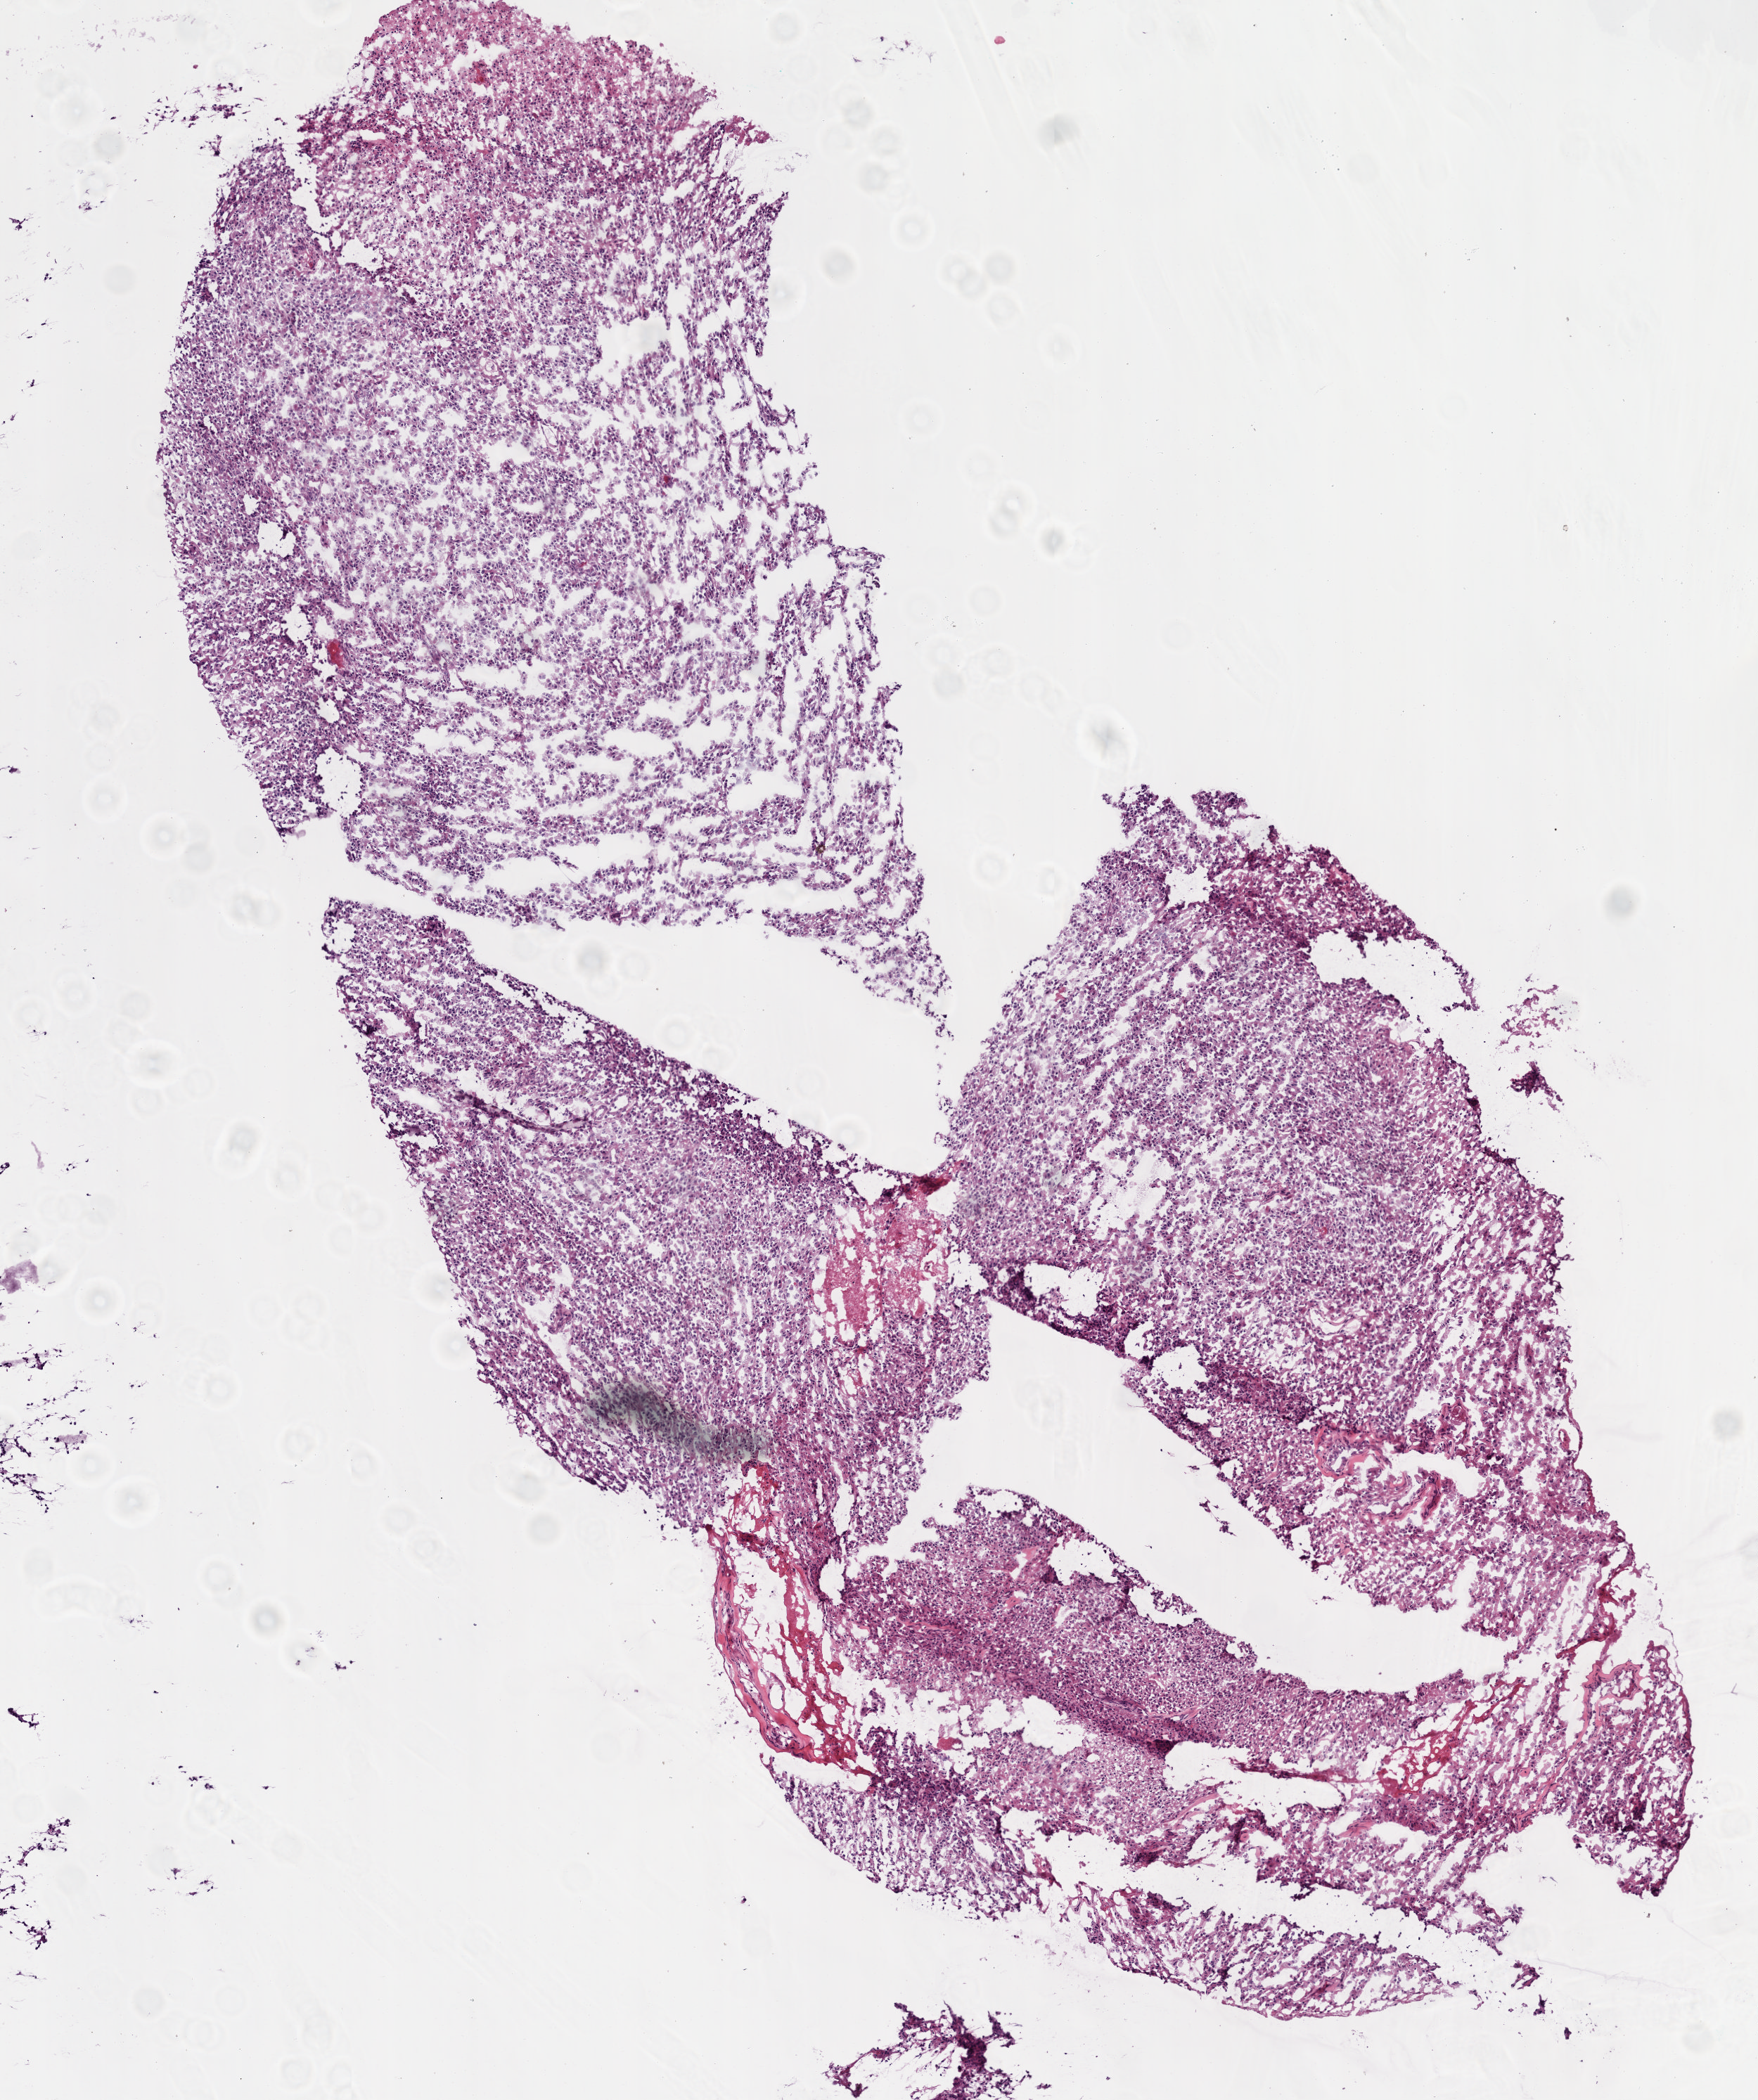
Whole-slide histology image, H&E-stained, low-resolution overview of the scanned area, about 5.0 x 6.0 mm (slide scanned at 20x). Frozen section. Brain, primary tumour sample. Female patient; age at initial diagnosis 66 years. Slide review estimates, as recorded: tumour cells 80%, tumour nuclei 95%, normal cells 0%, stromal cells 0%, necrosis 20%.
Histologic diagnosis: Glioblastoma.